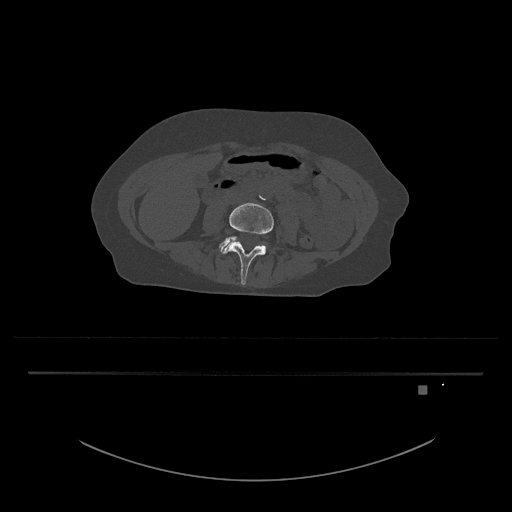
CT including the spine, one axial slice. Position 354 of 797 along the scan axis. 120 kVp. Bone window (W 1800 / L 400 HU). 512 × 512 image matrix, field of view 500 × 500 mm. Female patient, age 57 years. From the clinical record (not read from this slice): primary cancer: cervical.
Annotated regions visible in this slice (semi-automatic segmentation, software-assisted and operator-edited):
- L4 vertebra: bounding box <221,203,274,285> (left, top, right, bottom; pixels)